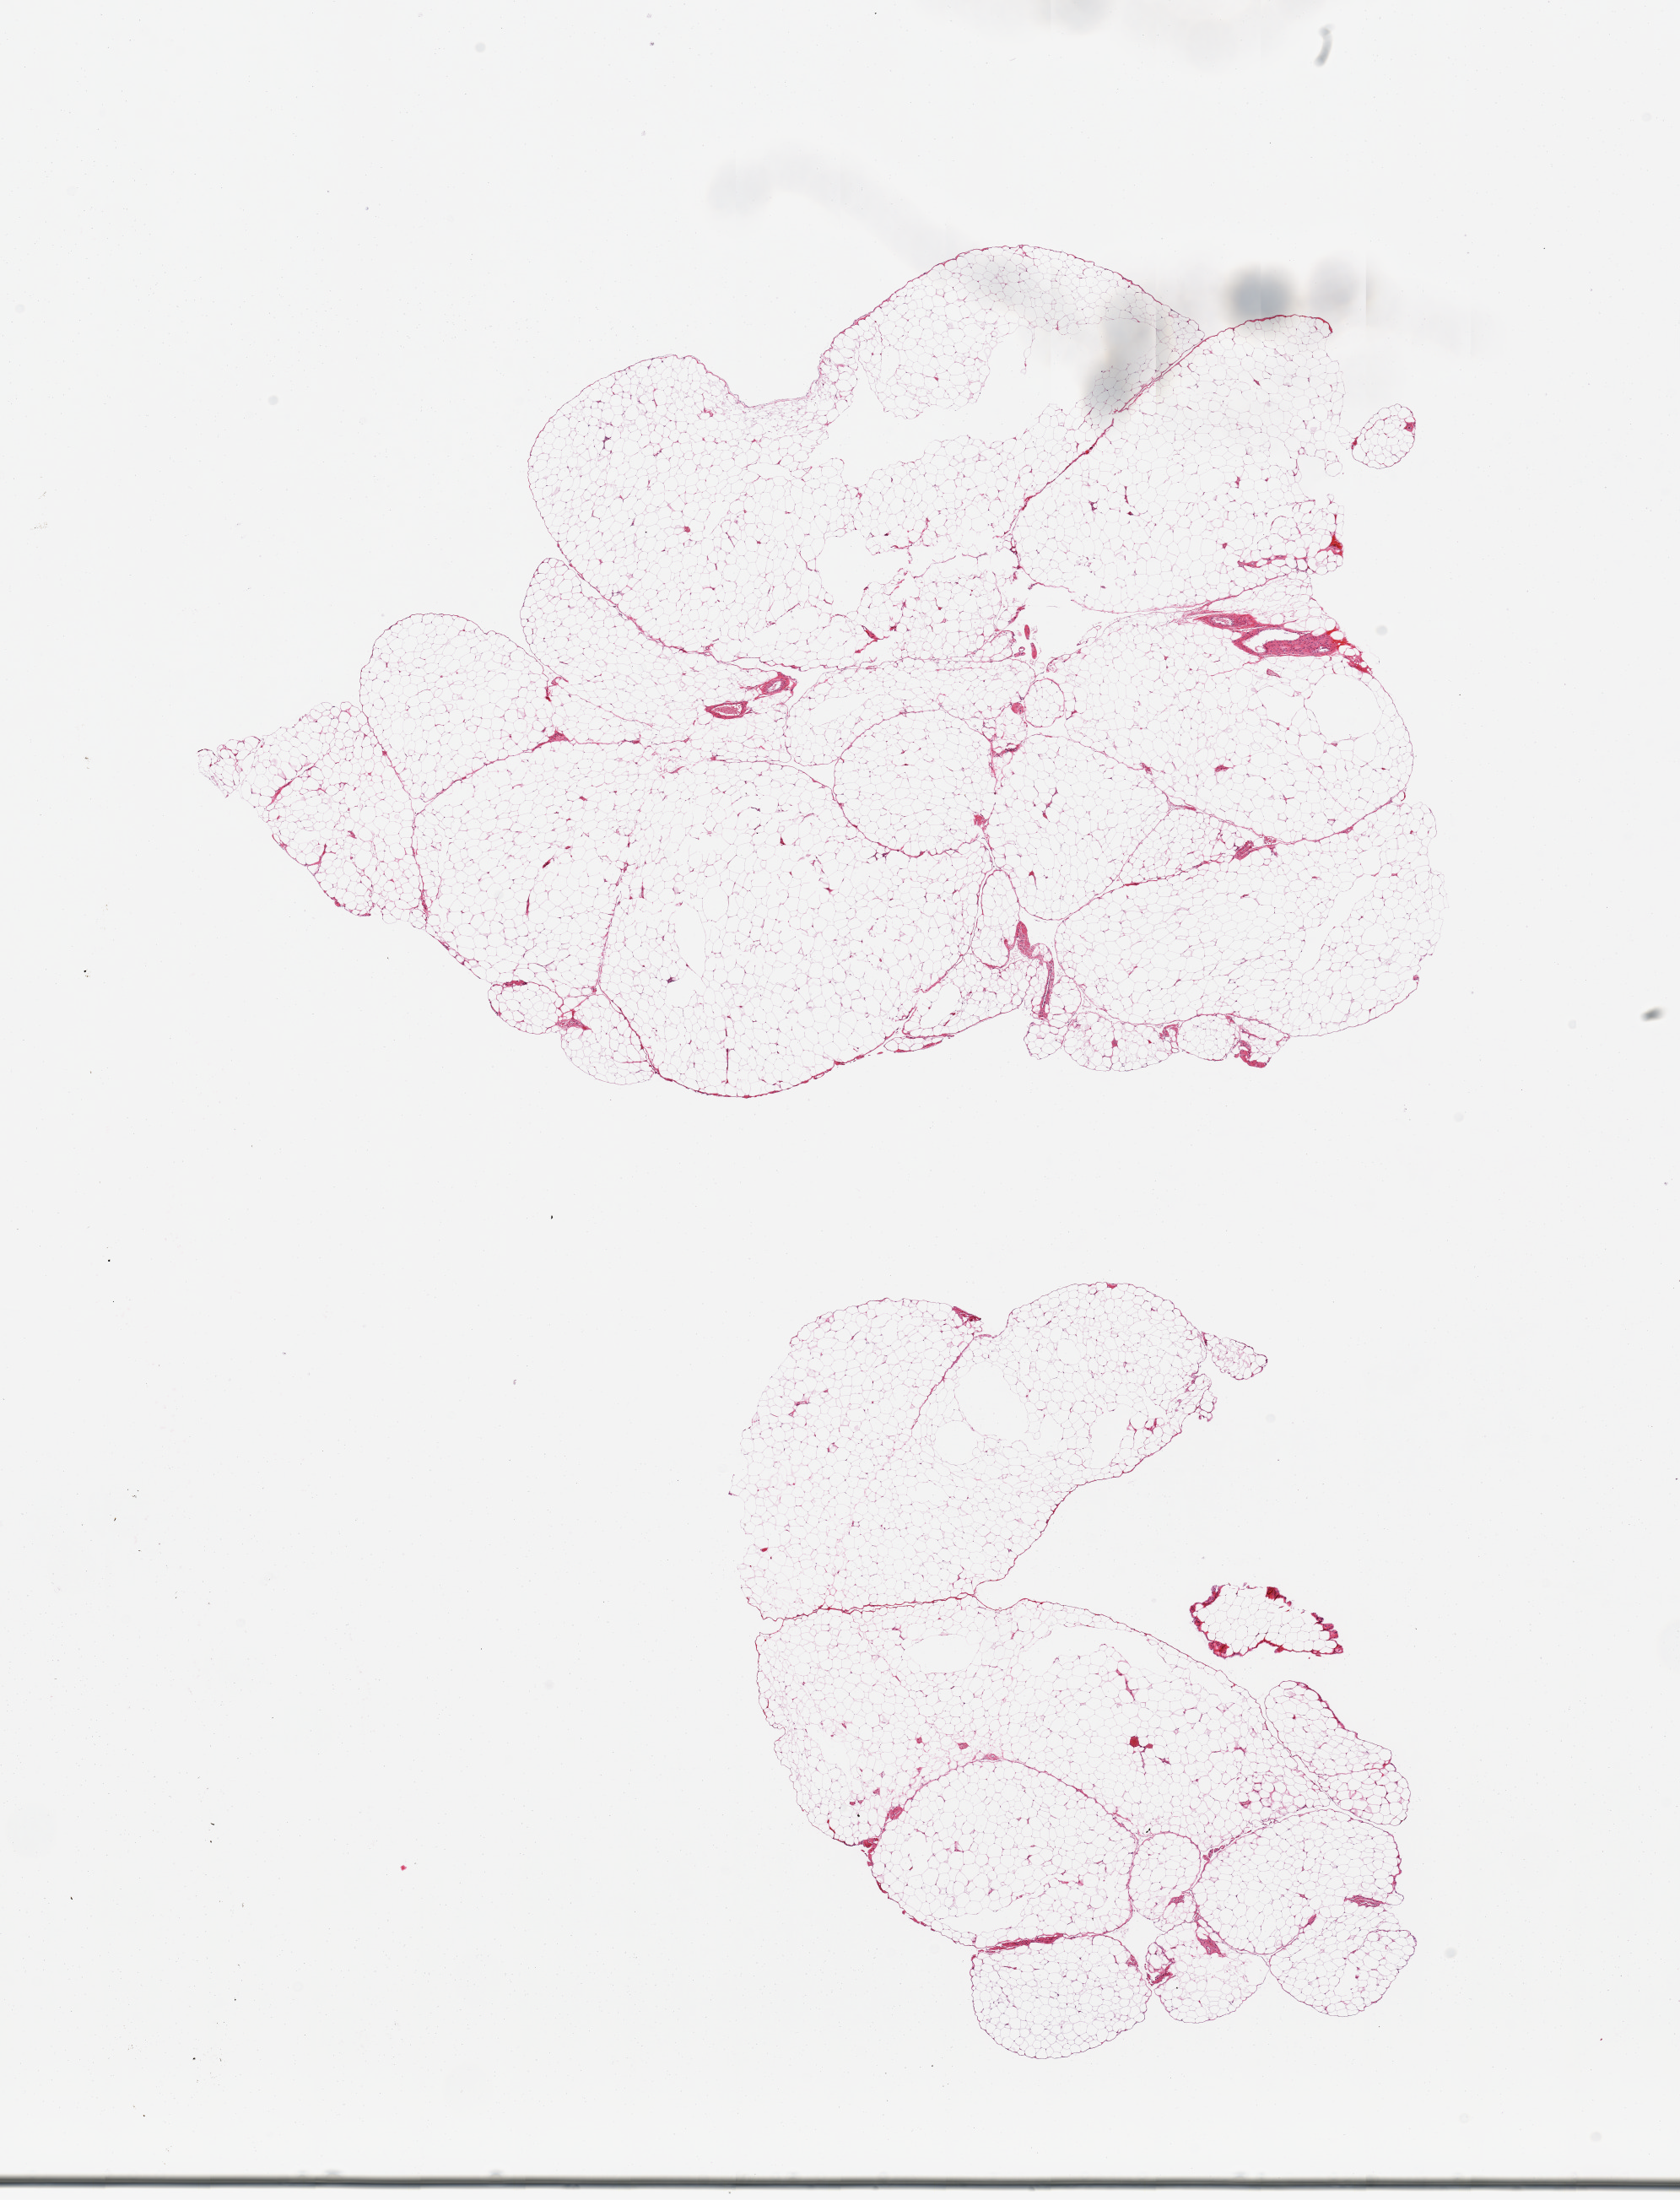
Digitized hematoxylin and eosin (H&E)-stained section, low-resolution overview of the scanned area, about 15.8 x 20.6 mm, PAXgene-fixed, paraffin-embedded tissue, target tissue: omentum, donor tissue sample. Male donor.
* review note (as recorded): 2 pieces